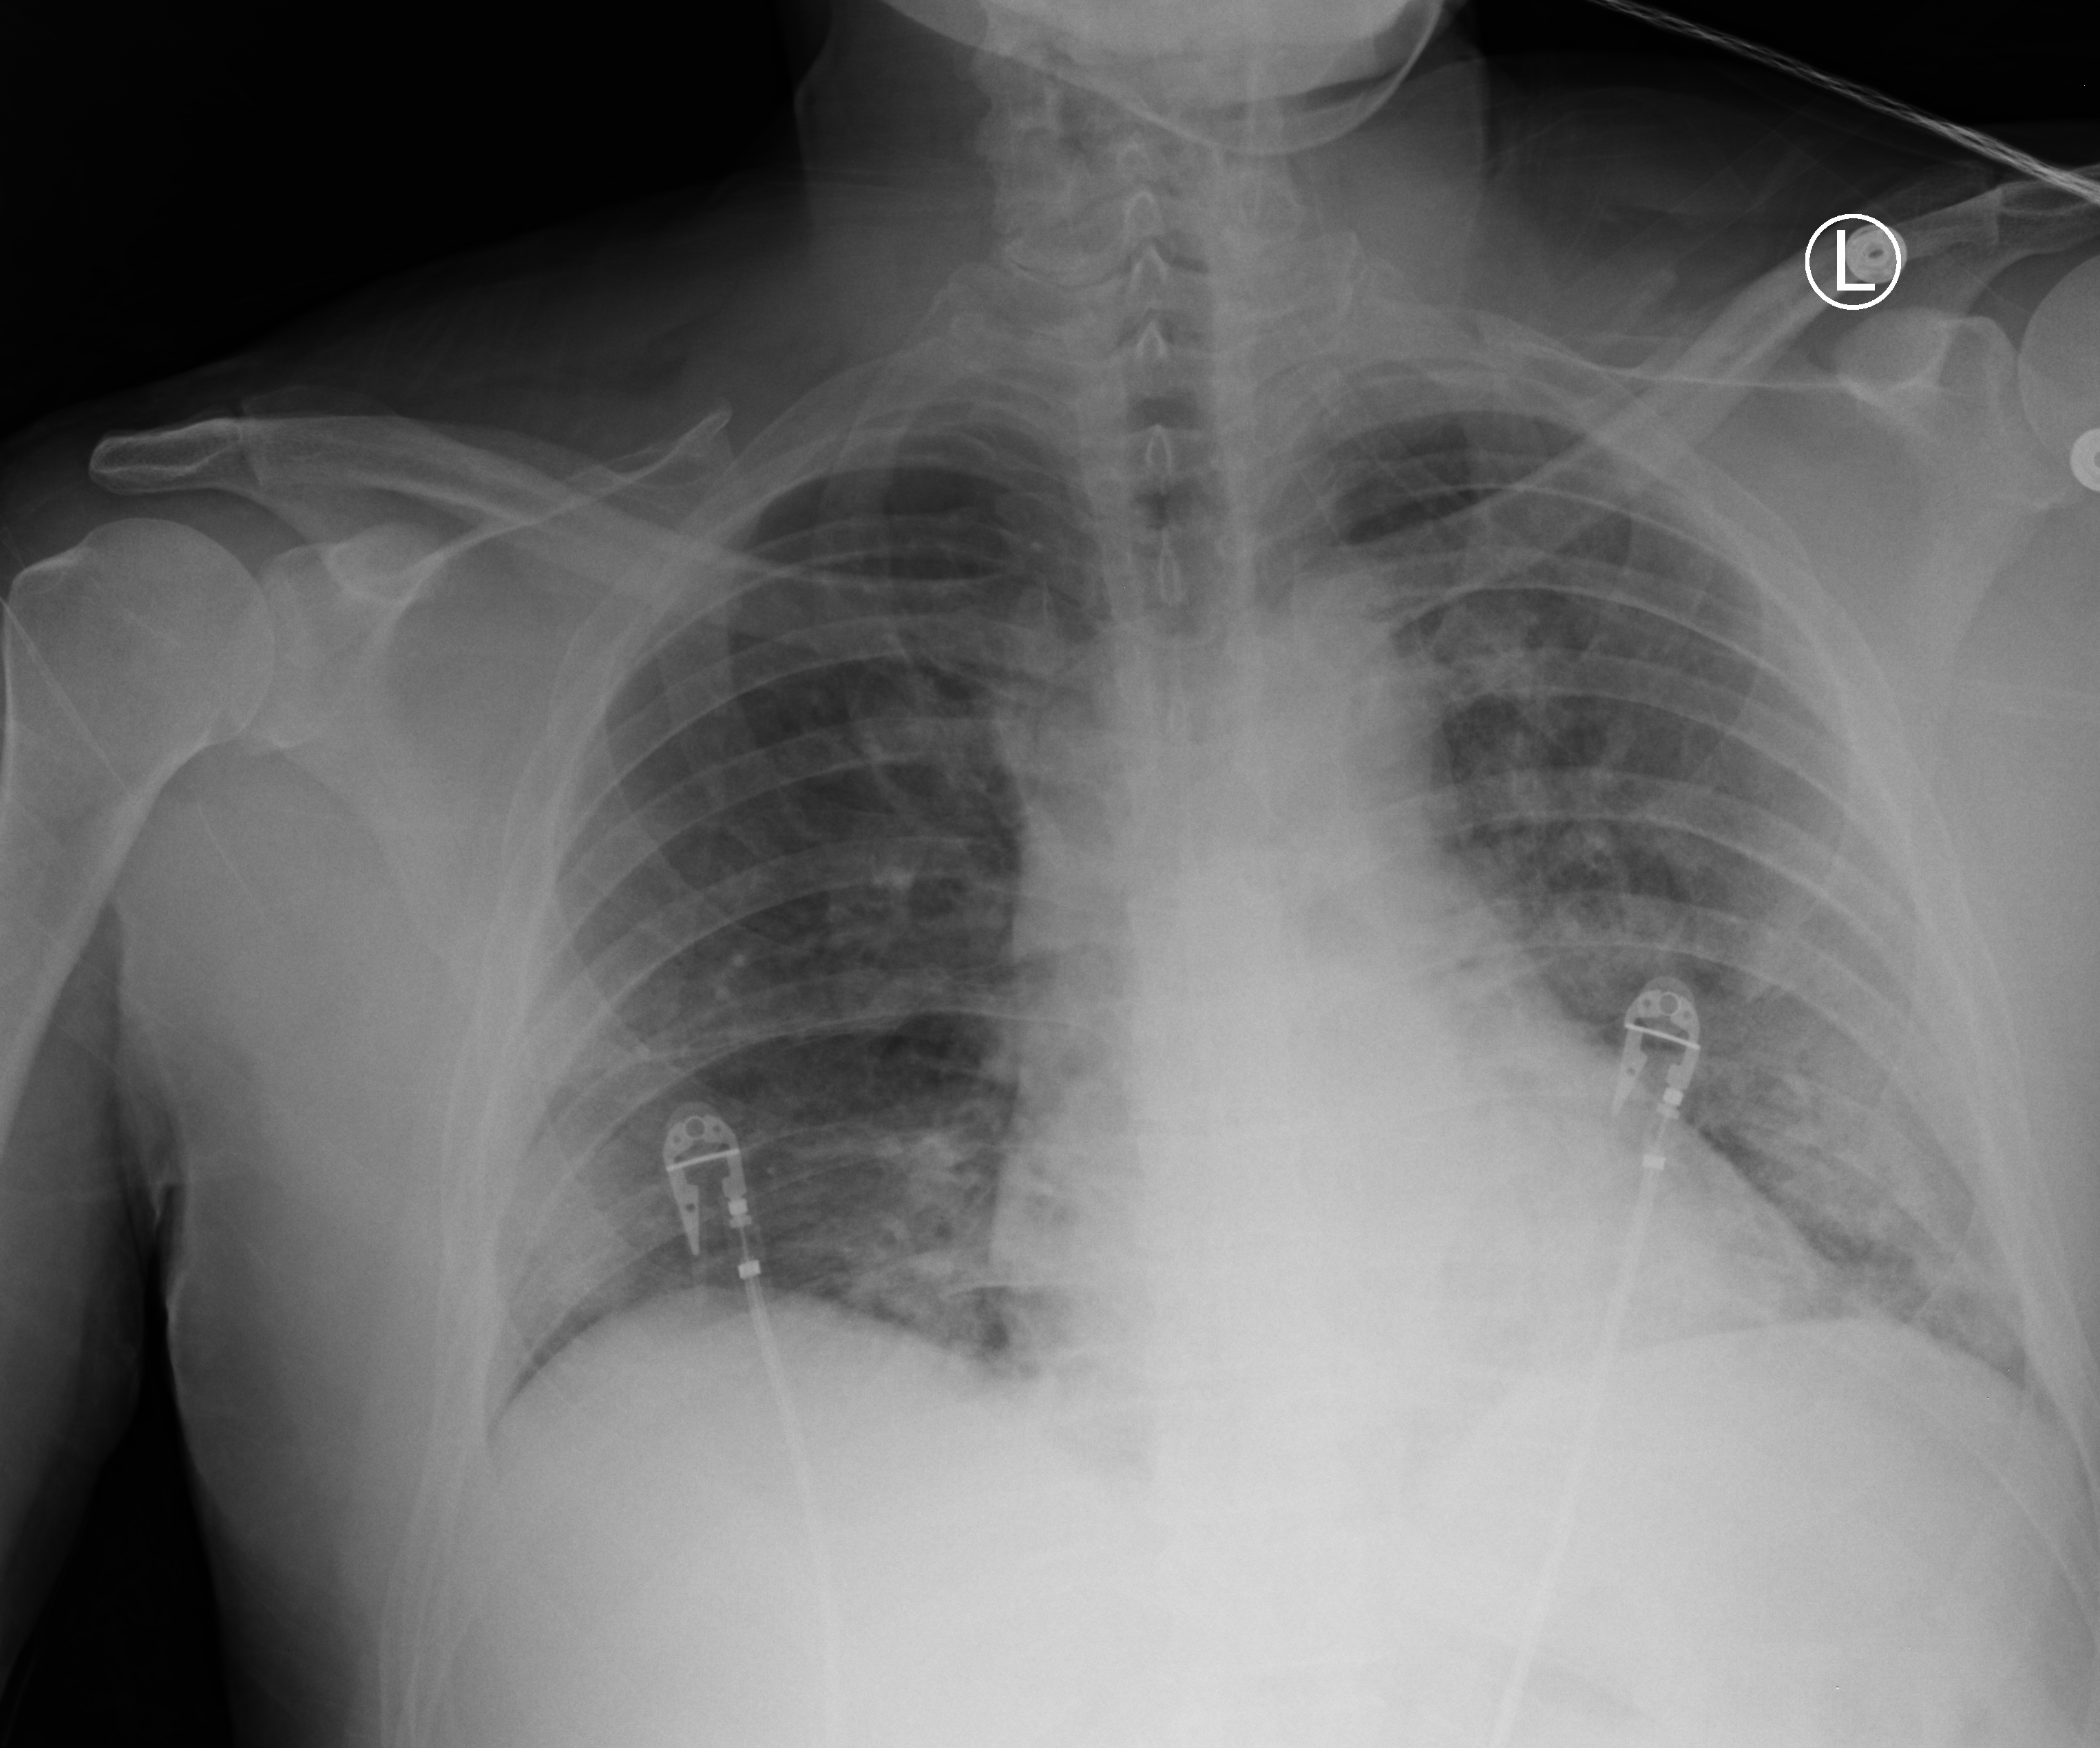
Portable chest radiograph; anteroposterior (AP) projection. Patient hospitalised with COVID-19; male, aged 18–59 years.
From the hospital-stay record, not from the radiograph (when in the stay this image was taken is not recorded): diabetes (admission record): no; admitted to intensive care during this hospital stay: yes.